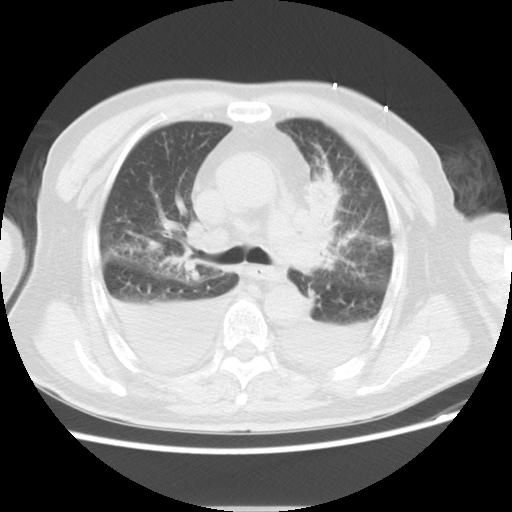
Chest CT, one axial slice. Position 15 of 21 along the scan axis. Lung window (W 1500 / L -600 HU). 5 mm slice thickness. 512 × 512 image matrix, field of view 350 × 350 mm. Patient: male, 66 years. From the clinical record (not read from this slice): clinical TNM (as recorded): T1c N0 M0.
Annotated regions visible in this slice (rectangle marked by the reading radiologist):
- lung tumour (recorded histology: adenocarcinoma): bounding box (x1, y1, x2, y2) in pixels: (310, 171, 344, 238)